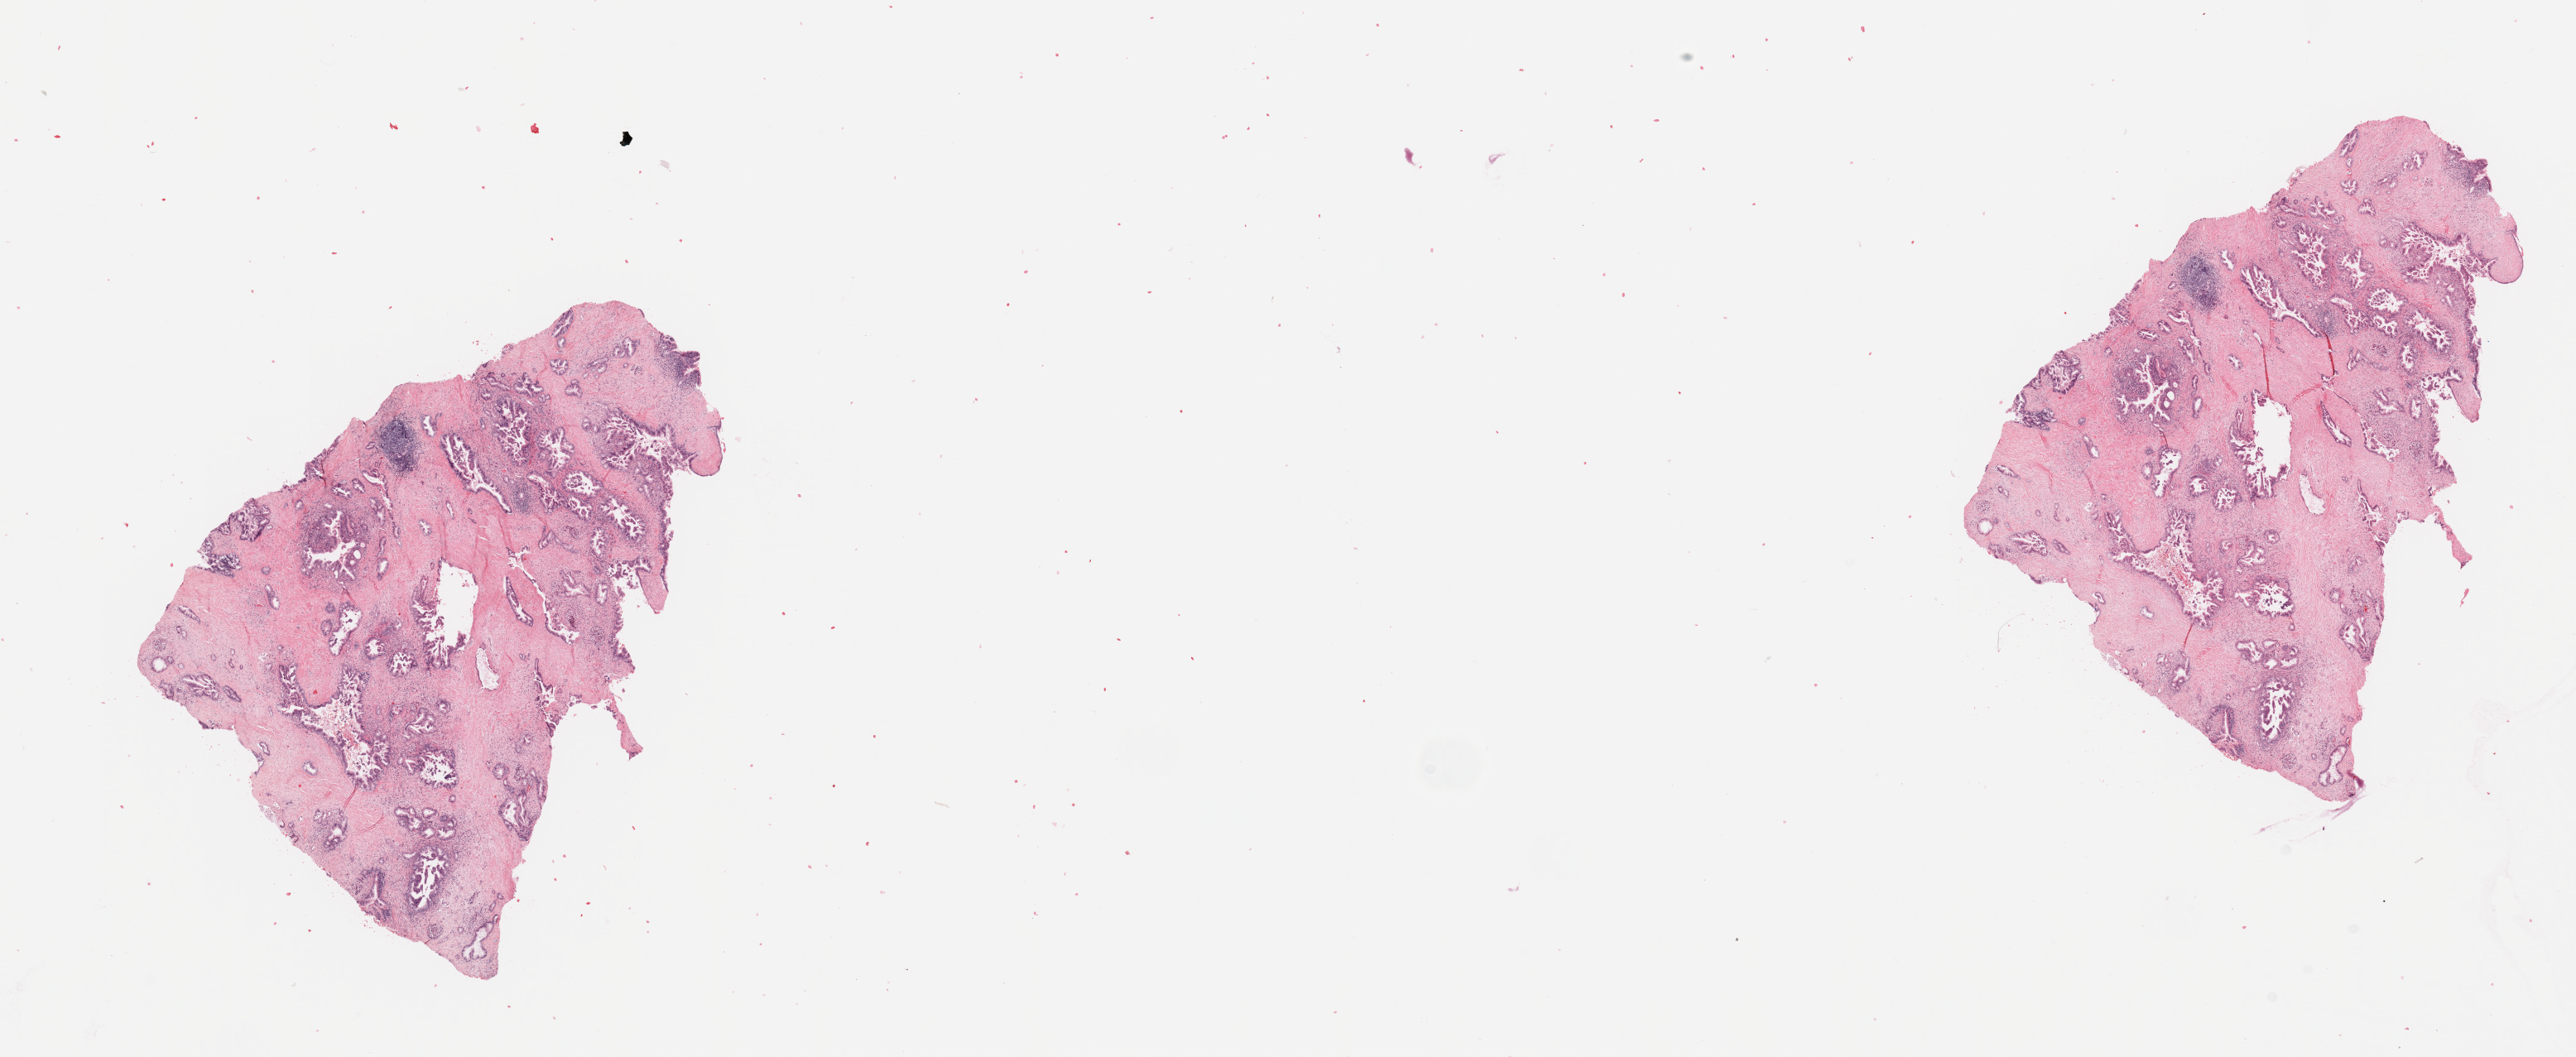
Digitized H&E tissue section (whole slide), shown as a low-resolution overview of the whole scanned area (about 24.6 x 10.1 mm), pancreas, tumour tissue. 71-year-old male patient. Histologic grade: G2 (moderately differentiated).
Primary tumour site (as recorded): body. Histologic diagnosis: Infiltrating duct carcinoma, NOS. AJCC pathologic stage: IIB.